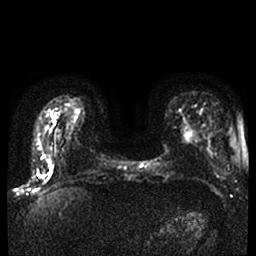
Breast MRI, one axial slice. Position 10 of 42 along the scan axis. Diffusion-weighted series; image 2 of 4 stored at this slice position (different b-values; order by instance number). 1.5 T. 4 mm slice thickness. 256 × 256 image matrix. Female patient.
Annotated regions visible in this slice (manually delineated by an expert):
- tumour on diffusion-weighted imaging: box from (x=45, y=172) to (x=51, y=182) px